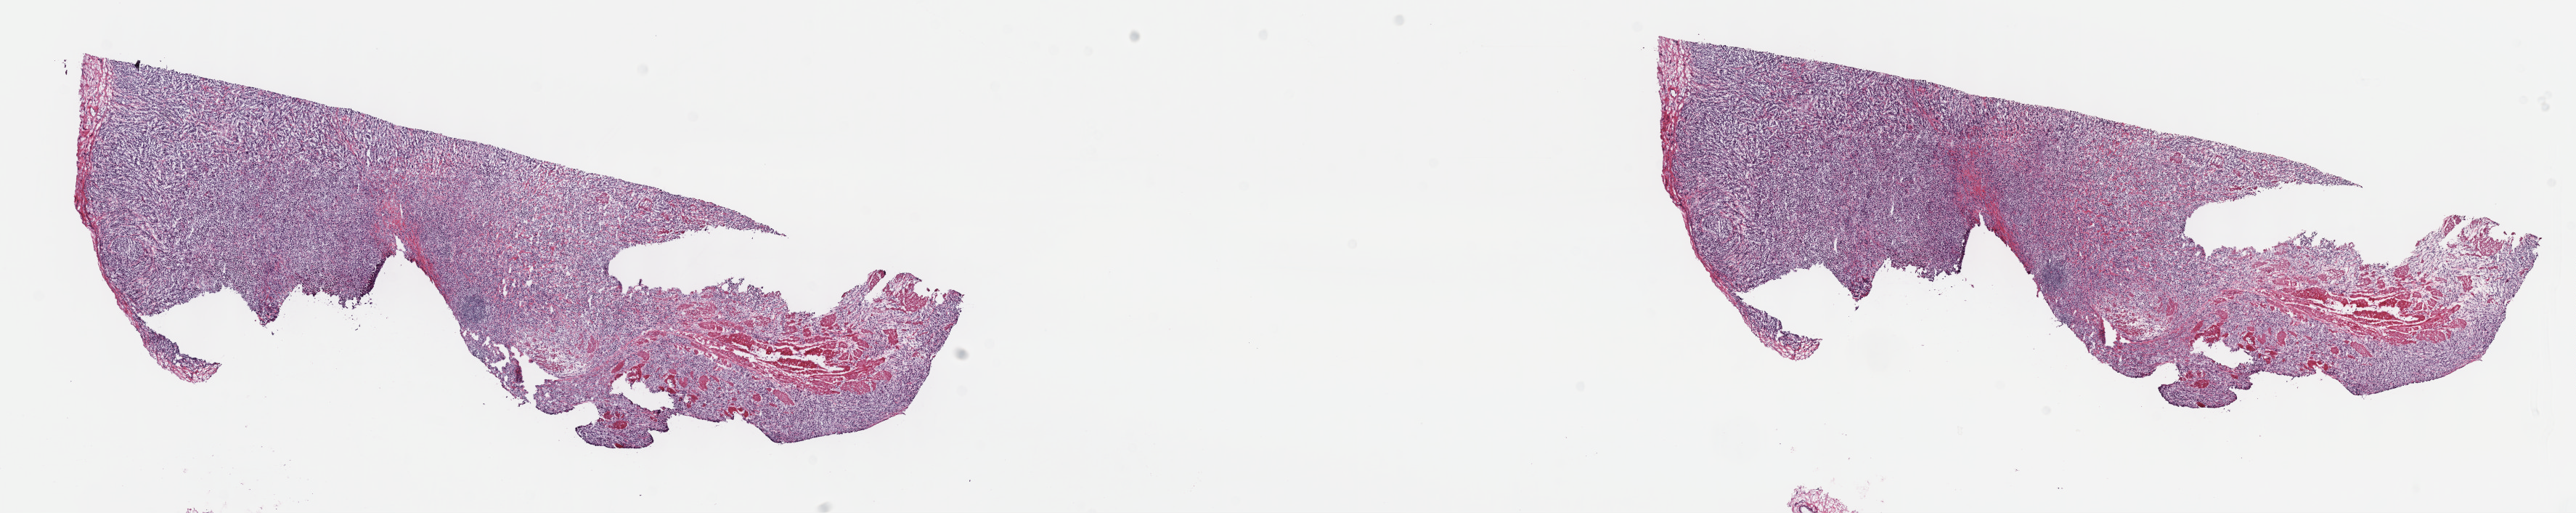
Digitized Hematoxylin and eosin (H&E) stained tissue section (whole slide), whole scanned area (about 28.7 x 5.7 mm) shown as a low-resolution overview; frozen section from the top of the tissue portion; bladder, primary tumour sample. Patient: male, age at initial diagnosis 68 years. Histologic grade: high grade. Composition of this section per pathologist review: tumour cells 85%, tumour nuclei 85%, normal cells 0%, stromal cells 15%, necrosis 0%. Inflammatory infiltration, as recorded: lymphocyte infiltration 2%, monocyte infiltration 1%, neutrophil infiltration 4%.
Diagnosis: Transitional cell carcinoma. AJCC pathologic stage: IV. Lymph nodes positive (case pathology): 30 of 53 examined.